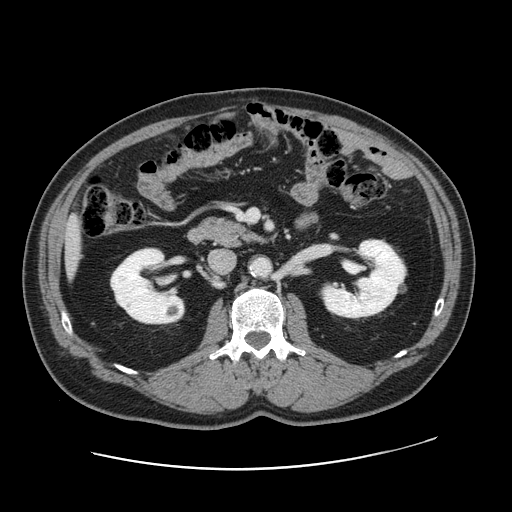
Contrast-enhanced abdominal CT, one axial slice. Position 65 of 178 along the scan axis. Intravenous contrast given. Soft-tissue window (W 400 / L 40 HU). 2.5 mm slice thickness. 512 × 512 image matrix. Male patient, age 63 years. Case-level facts recorded for this patient, not image findings: diagnosis: colorectal cancer liver metastases, imaged before liver resection; multiple liver metastases: yes; largest metastasis: 8 cm; chemotherapy before resection: no.
Annotated regions visible in this slice (expert manual segmentation):
- liver: box from (x=66, y=222) to (x=81, y=265) px